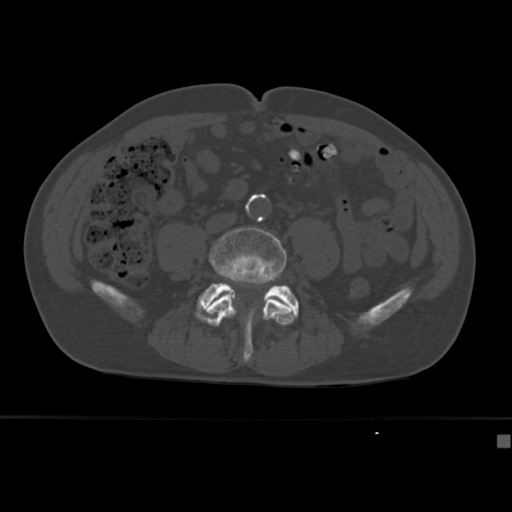
CT including the spine, one axial slice; position 98 of 430 along the scan axis; bone window (W 1800 / L 400 HU); 1.5 mm slice thickness; 512 × 512 image matrix, field of view 337 × 337 mm. Male patient, age 64 years. From the clinical record (not read from this slice): primary cancer: uterus; vertebrae with lytic lesions (as recorded): T1, T4, T5, T7, L5.
Outlined on this slice (semi-automatic segmentation, software-assisted and operator-edited):
- L4 vertebra: bounding box (x1, y1, x2, y2) in pixels: (204, 227, 294, 351)
- L5 vertebra: (197, 283, 299, 362)